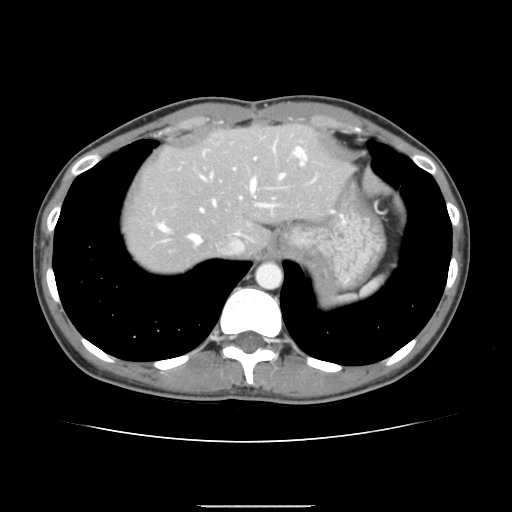
Contrast-enhanced abdominal CT, one axial slice; slice 121 of 150 in the series (ordered by position); soft-tissue window (W 400 / L 40 HU); 512 × 512 image matrix. Female patient, age 32 years. Case-level facts recorded for this patient, not image findings: diagnosis: colorectal cancer liver metastases, imaged before liver resection; multiple liver metastases: yes; largest metastasis: 0.7 cm; disease in both lobes: no.
Annotated regions visible in this slice (manually delineated by an expert):
- hepatic veins: bounding box (x1, y1, x2, y2) in pixels: (158, 151, 296, 253)
- liver: (124, 125, 349, 272)
- planned liver remnant (the part of the liver to remain after resection): (124, 126, 350, 258)
- portal vein (with intrahepatic branches): (200, 143, 315, 212)